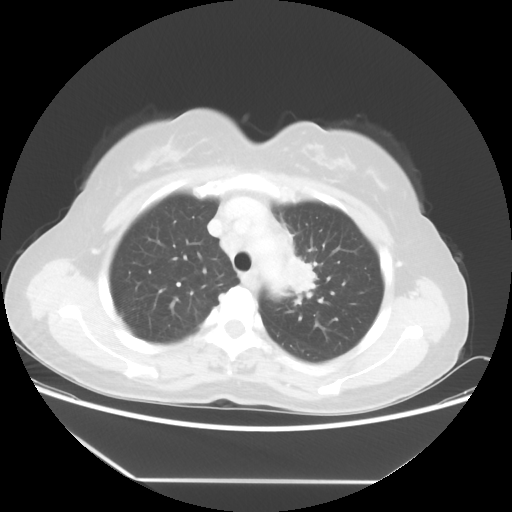
Chest CT, one axial slice. Slice 40 of 52 in the series (ordered by position). Lung window (W 1500 / L -600 HU). 512 × 512 image matrix. Female patient, age 50 years. Case-level facts recorded for this patient, not image findings: clinical TNM (as recorded): T2 N3 M0.
Annotated regions visible in this slice (rectangle marked by the reading radiologist):
- lung tumour (recorded histology: adenocarcinoma): bounding box [x1, y1, x2, y2] px = [278, 251, 325, 302]